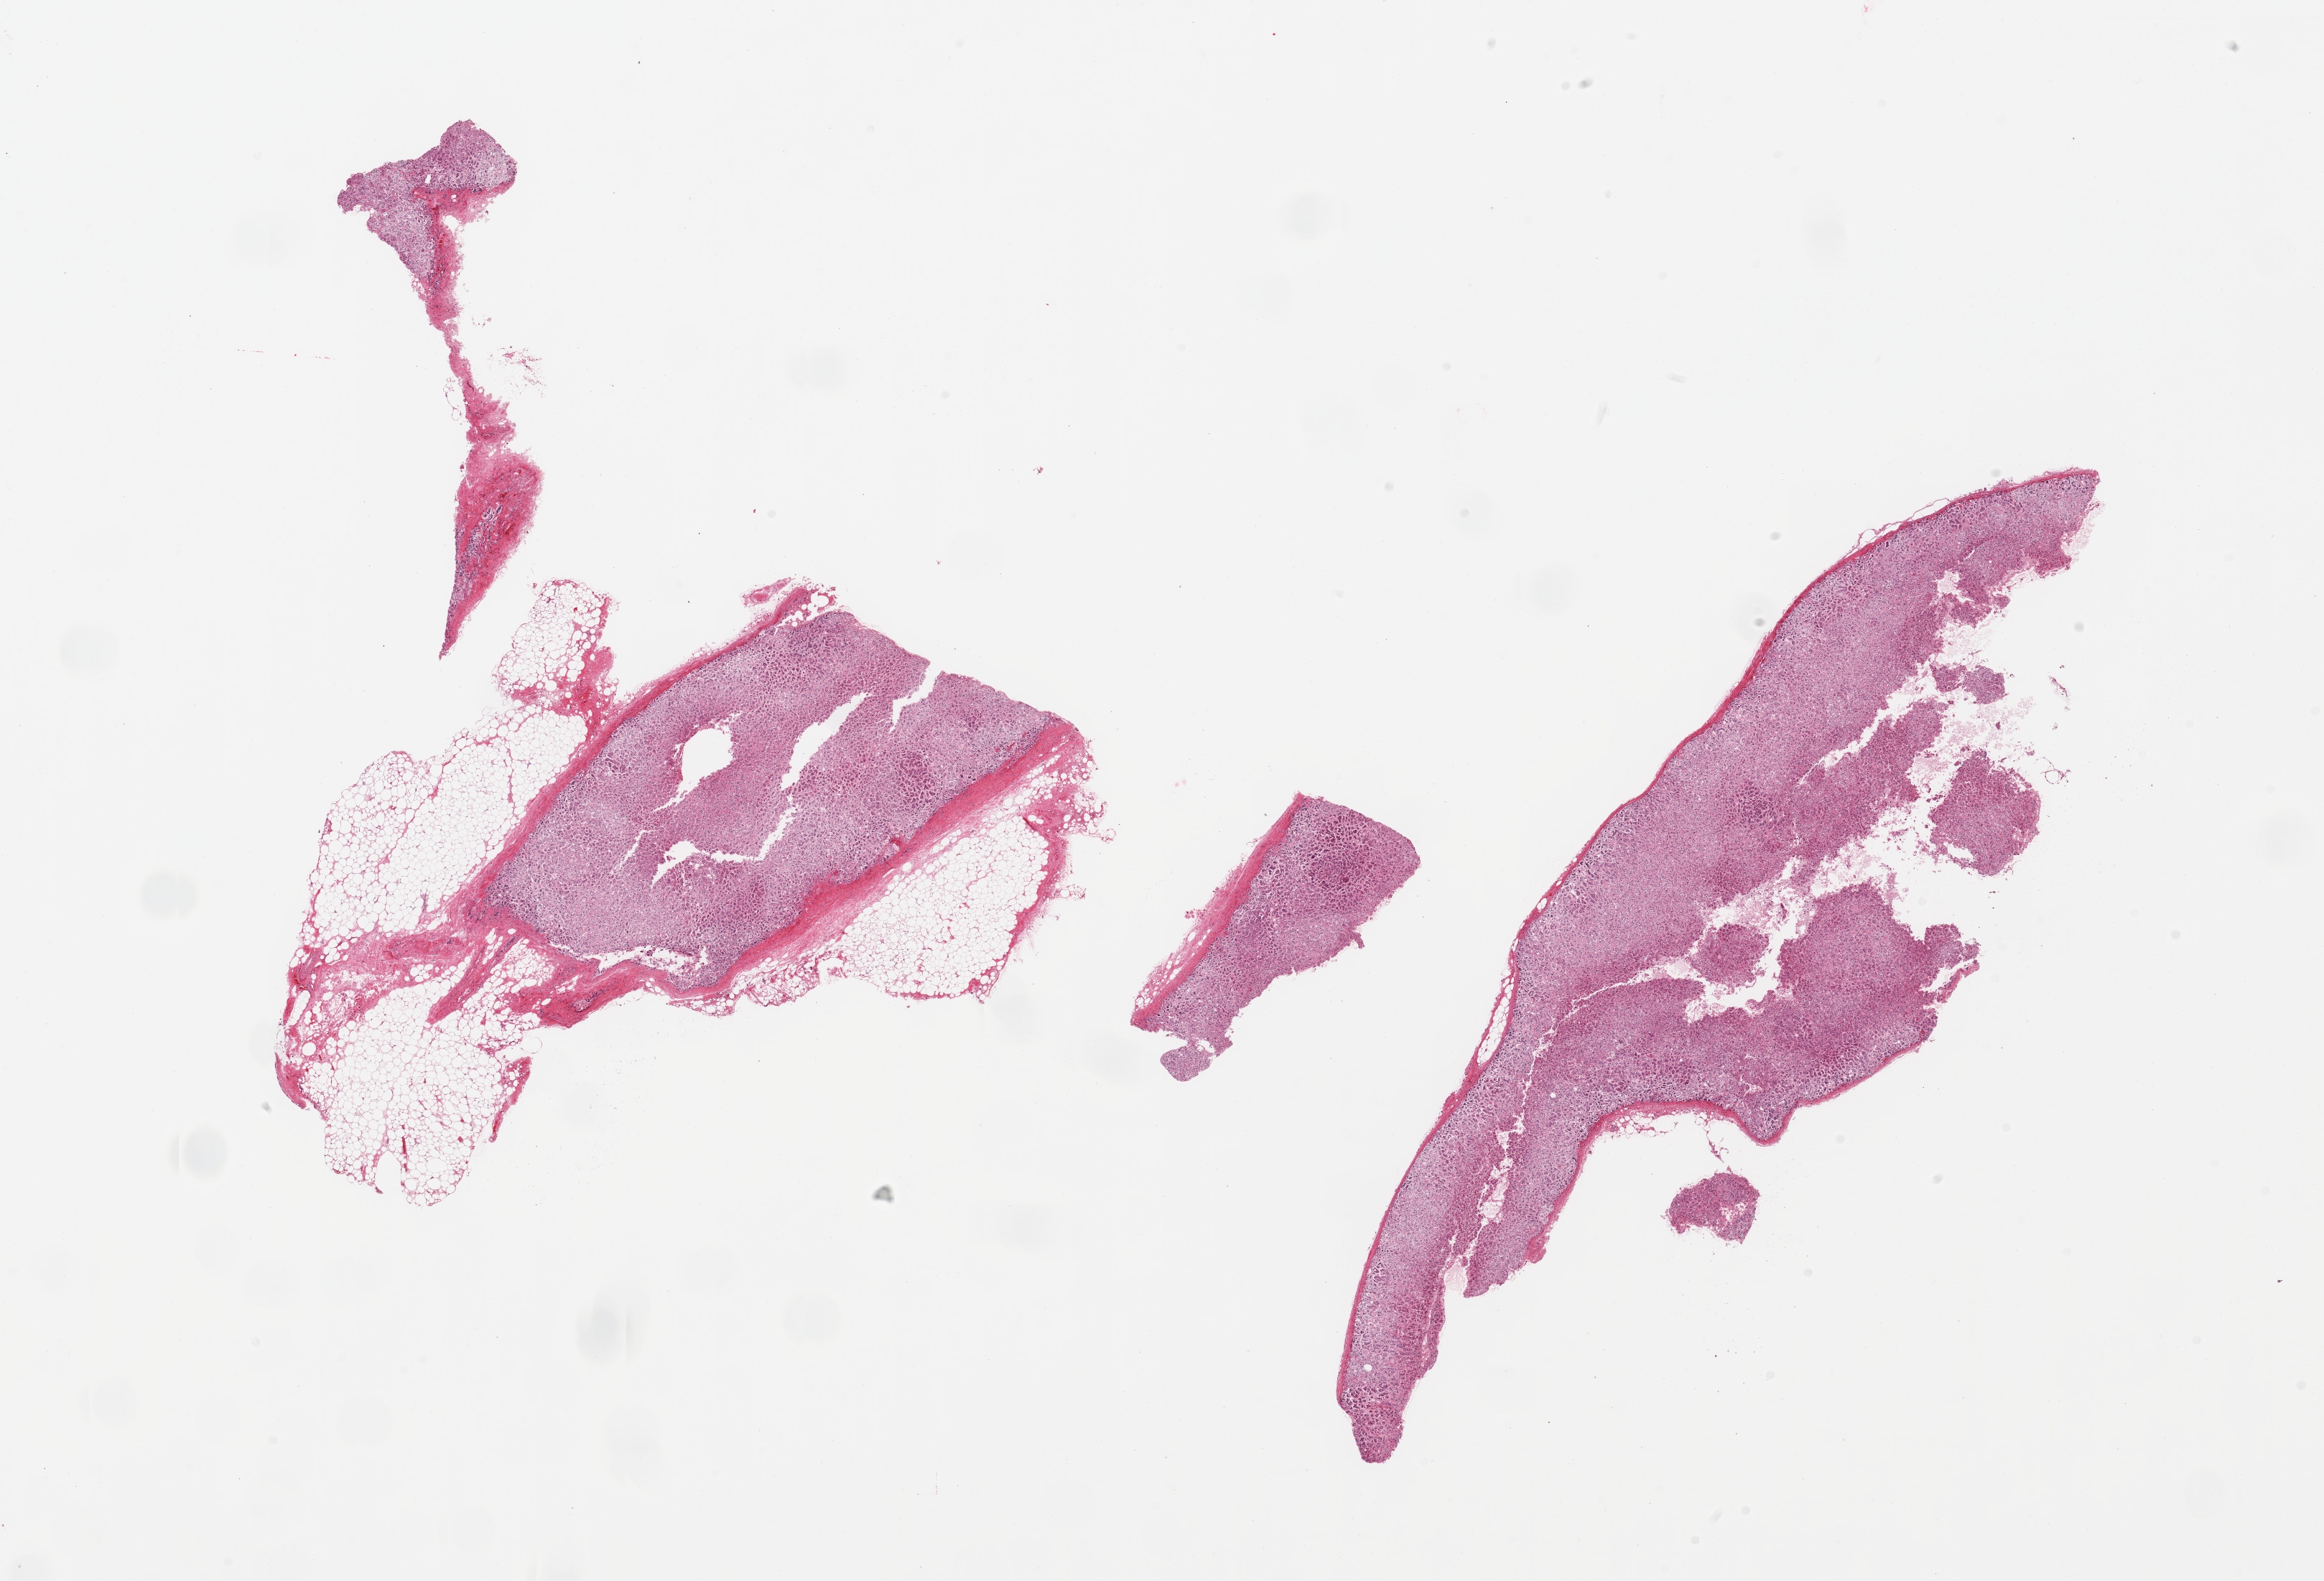
Whole-slide image, haematoxylin and eosin stain, shown as a low-resolution overview of the whole scanned area (about 25.6 x 17.4 mm, from a 20x scan); PAXgene-fixed, paraffin-embedded tissue; section of adrenal gland (target tissue); donor tissue sample.
Pathologist's review note for this sample: 2 pieces, cortex; Adherent fat is ~20% of specimen.